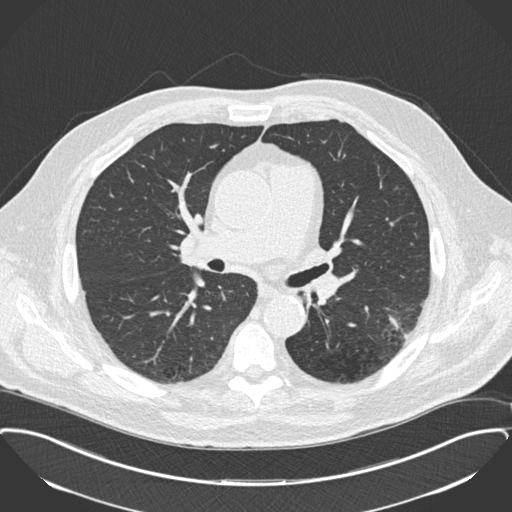
Low-dose screening chest CT, one axial slice; position 100 of 175 along the scan axis; reconstruction kernel B30f; 120 kVp; lung window (W 1500 / L -600 HU); 2 mm slice thickness; 512 × 512 image matrix, field of view 400 × 400 mm.
Outlined on this slice (expert manual segmentation):
- lesion 1 (tumor, lower lobe of left lung): bounding box (x1, y1, x2, y2) in pixels: (389, 316, 408, 339)